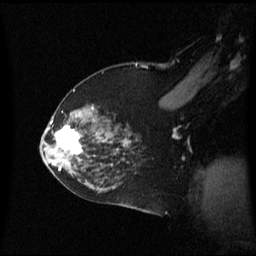
Breast MRI (dynamic contrast-enhanced), one sagittal slice. Position 42 of 60 along the scan axis. Dynamic contrast-enhanced series, image 2 of 3 at this slice position (ordered by acquisition). 1.5 T. TE 4.2 ms, TR 8.4 ms. 2 mm slice thickness. 256 × 256 image matrix, field of view 240 × 240 mm. Female patient, age 59 years. Case-level facts recorded for this patient, not image findings: setting: breast cancer imaged before/during neoadjuvant chemotherapy; receptor status: HR-positive, HER2-negative.
Outlined on this slice (semi-automatically segmented with operator editing):
- analysis volume of interest (the breast-tissue region the enhancement analysis was run in; not a lesion): box from (x=46, y=114) to (x=89, y=163) px
- tumour enhancement mask (voxels above the 70 % enhancement threshold inside the analysis volume of interest): (x=55, y=126)–(x=82, y=155)